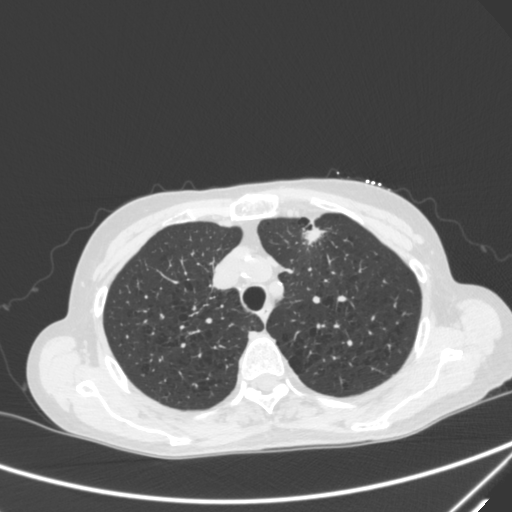
Chest CT, one axial slice. Slice 235 of 300 in the series (ordered by position). Lung window (W 1500 / L -600 HU). 1 mm slice thickness. 512 × 512 image matrix, field of view 350 × 350 mm. Patient: female, 71 years. From the clinical record (not read from this slice): clinical TNM (as recorded): T1c N0 M0.
Outlined on this slice (bounding box drawn by a radiologist):
- lung tumour (recorded histology: adenocarcinoma): bounding box [x1, y1, x2, y2] px = [298, 224, 328, 250]